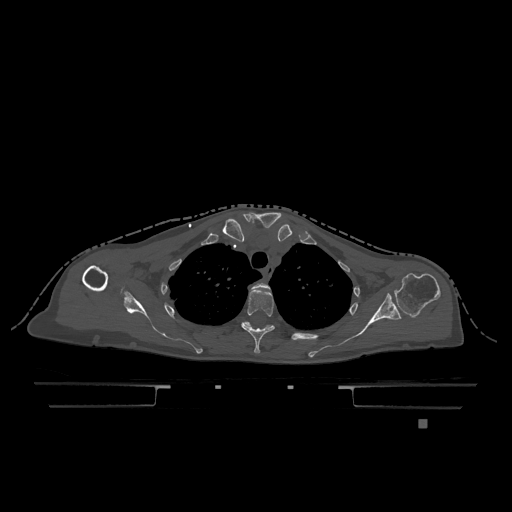
CT including the spine, one axial slice; position 919 of 1317 along the scan axis; bone window (W 1800 / L 400 HU); 0.5 mm slice thickness; 512 × 512 image matrix. Patient: female, 74 years. From the clinical record (not read from this slice): primary cancer: lung; vertebrae with lytic lesions (as recorded): T1, T4, T5, T6, L4, L5.
Annotated regions visible in this slice (semi-automatically segmented with operator editing):
- T2 vertebra: bounding box <251,282,270,291> (left, top, right, bottom; pixels)
- T3 vertebra: <241,289,275,353>
- T4 vertebra: <244,321,307,340>
- T6 vertebra: <256,290,259,292>